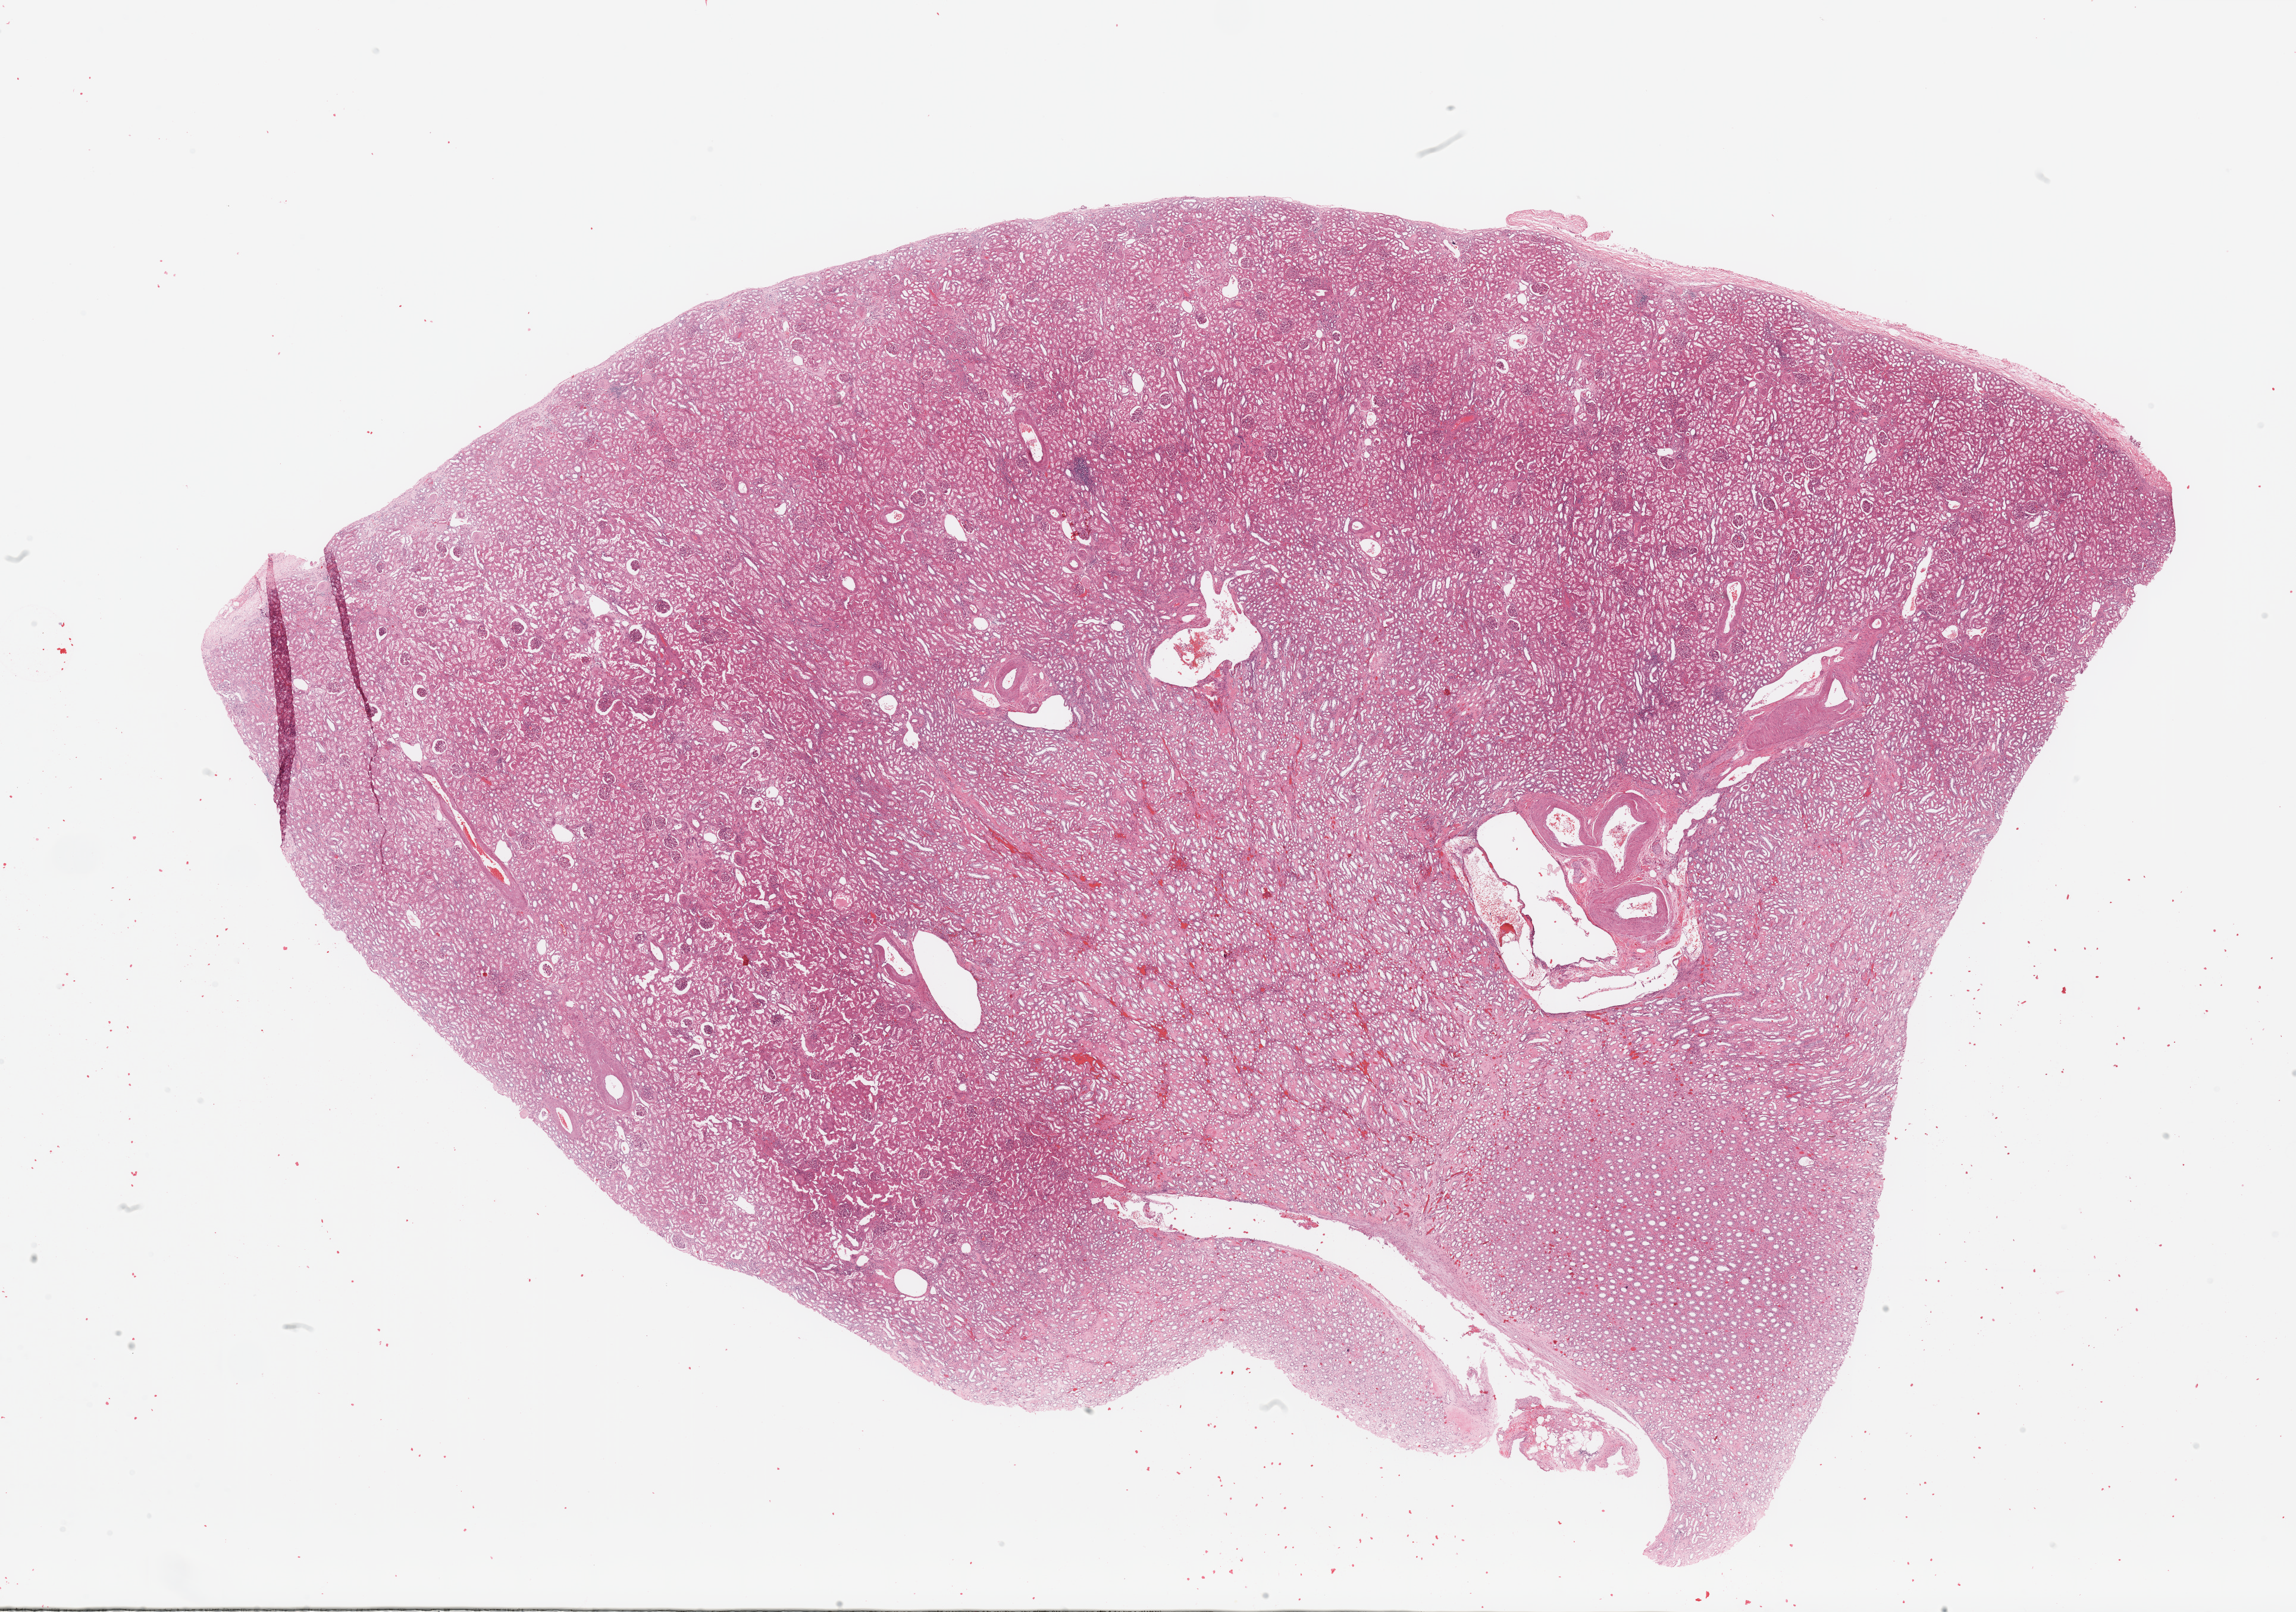
H&E whole-slide image, low-resolution overview of the scanned area, about 30.5 x 21.4 mm; normal (non-tumour) tissue sample, sampled site: kidney. Female, 76 y/o.
This section: normal (non-tumour) tissue from the same patient. Patient diagnosis: Renal cell carcinoma, NOS.